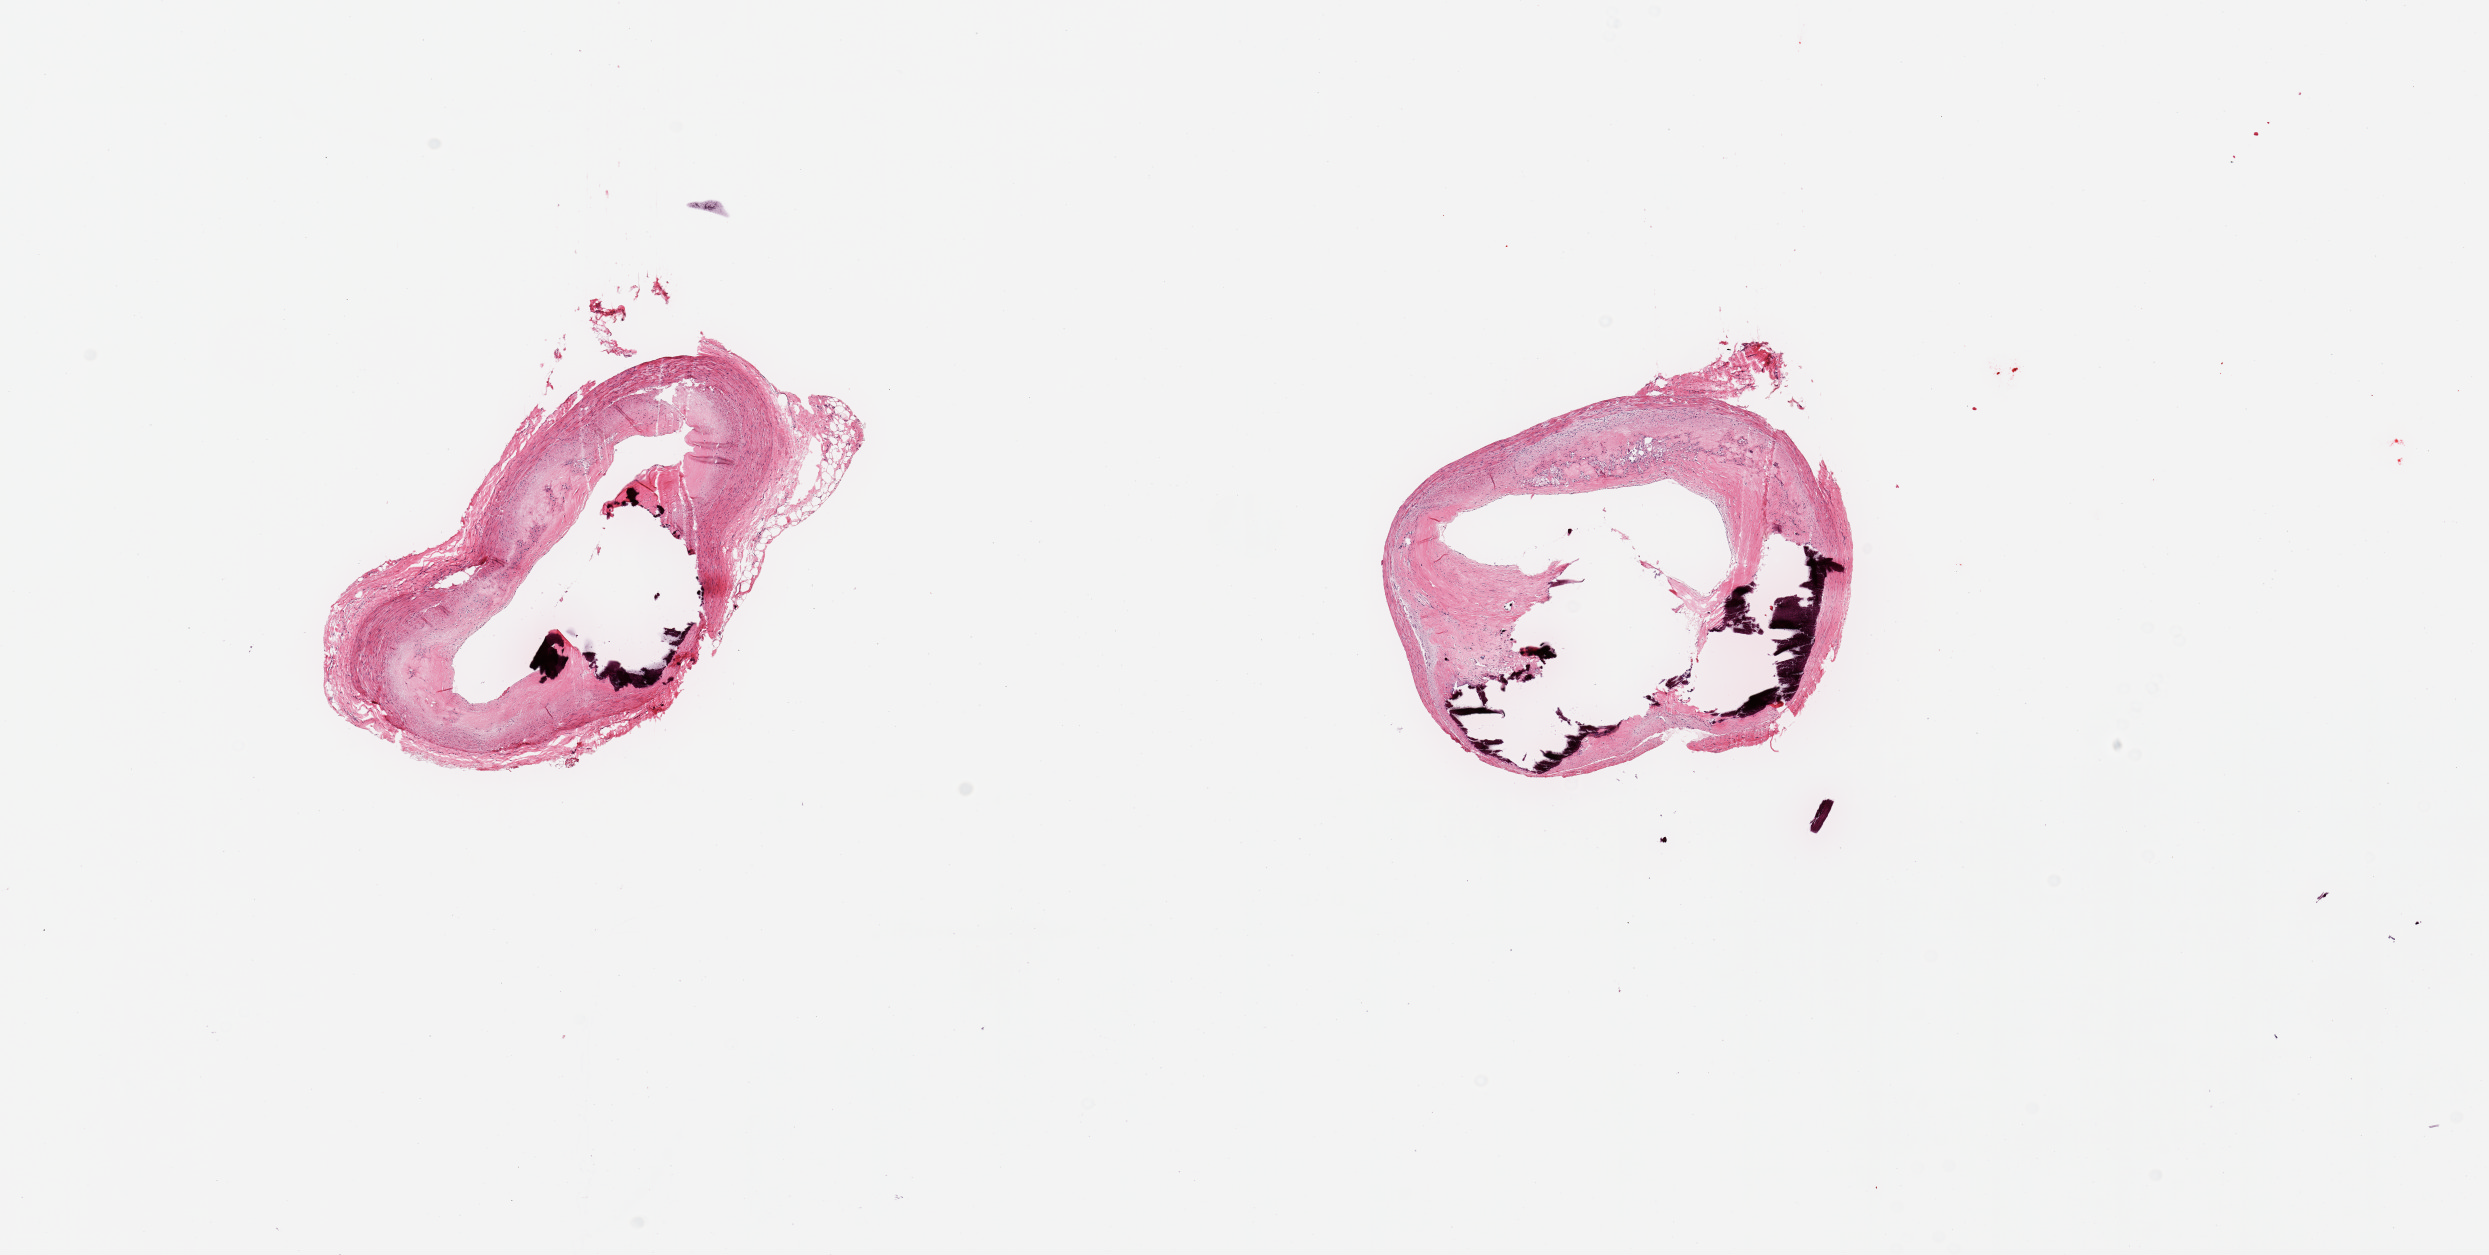
Whole-slide image, haematoxylin and eosin stain, low-resolution overview of the scanned area, about 19.7 x 9.9 mm; PAXgene-fixed paraffin-embedded (PFPE) section; section of coronary artery (target tissue); donor tissue sample. Donor: male.
Reviewer comment on this tissue sample: 2 pieces; severe calcific atherosclerosis.